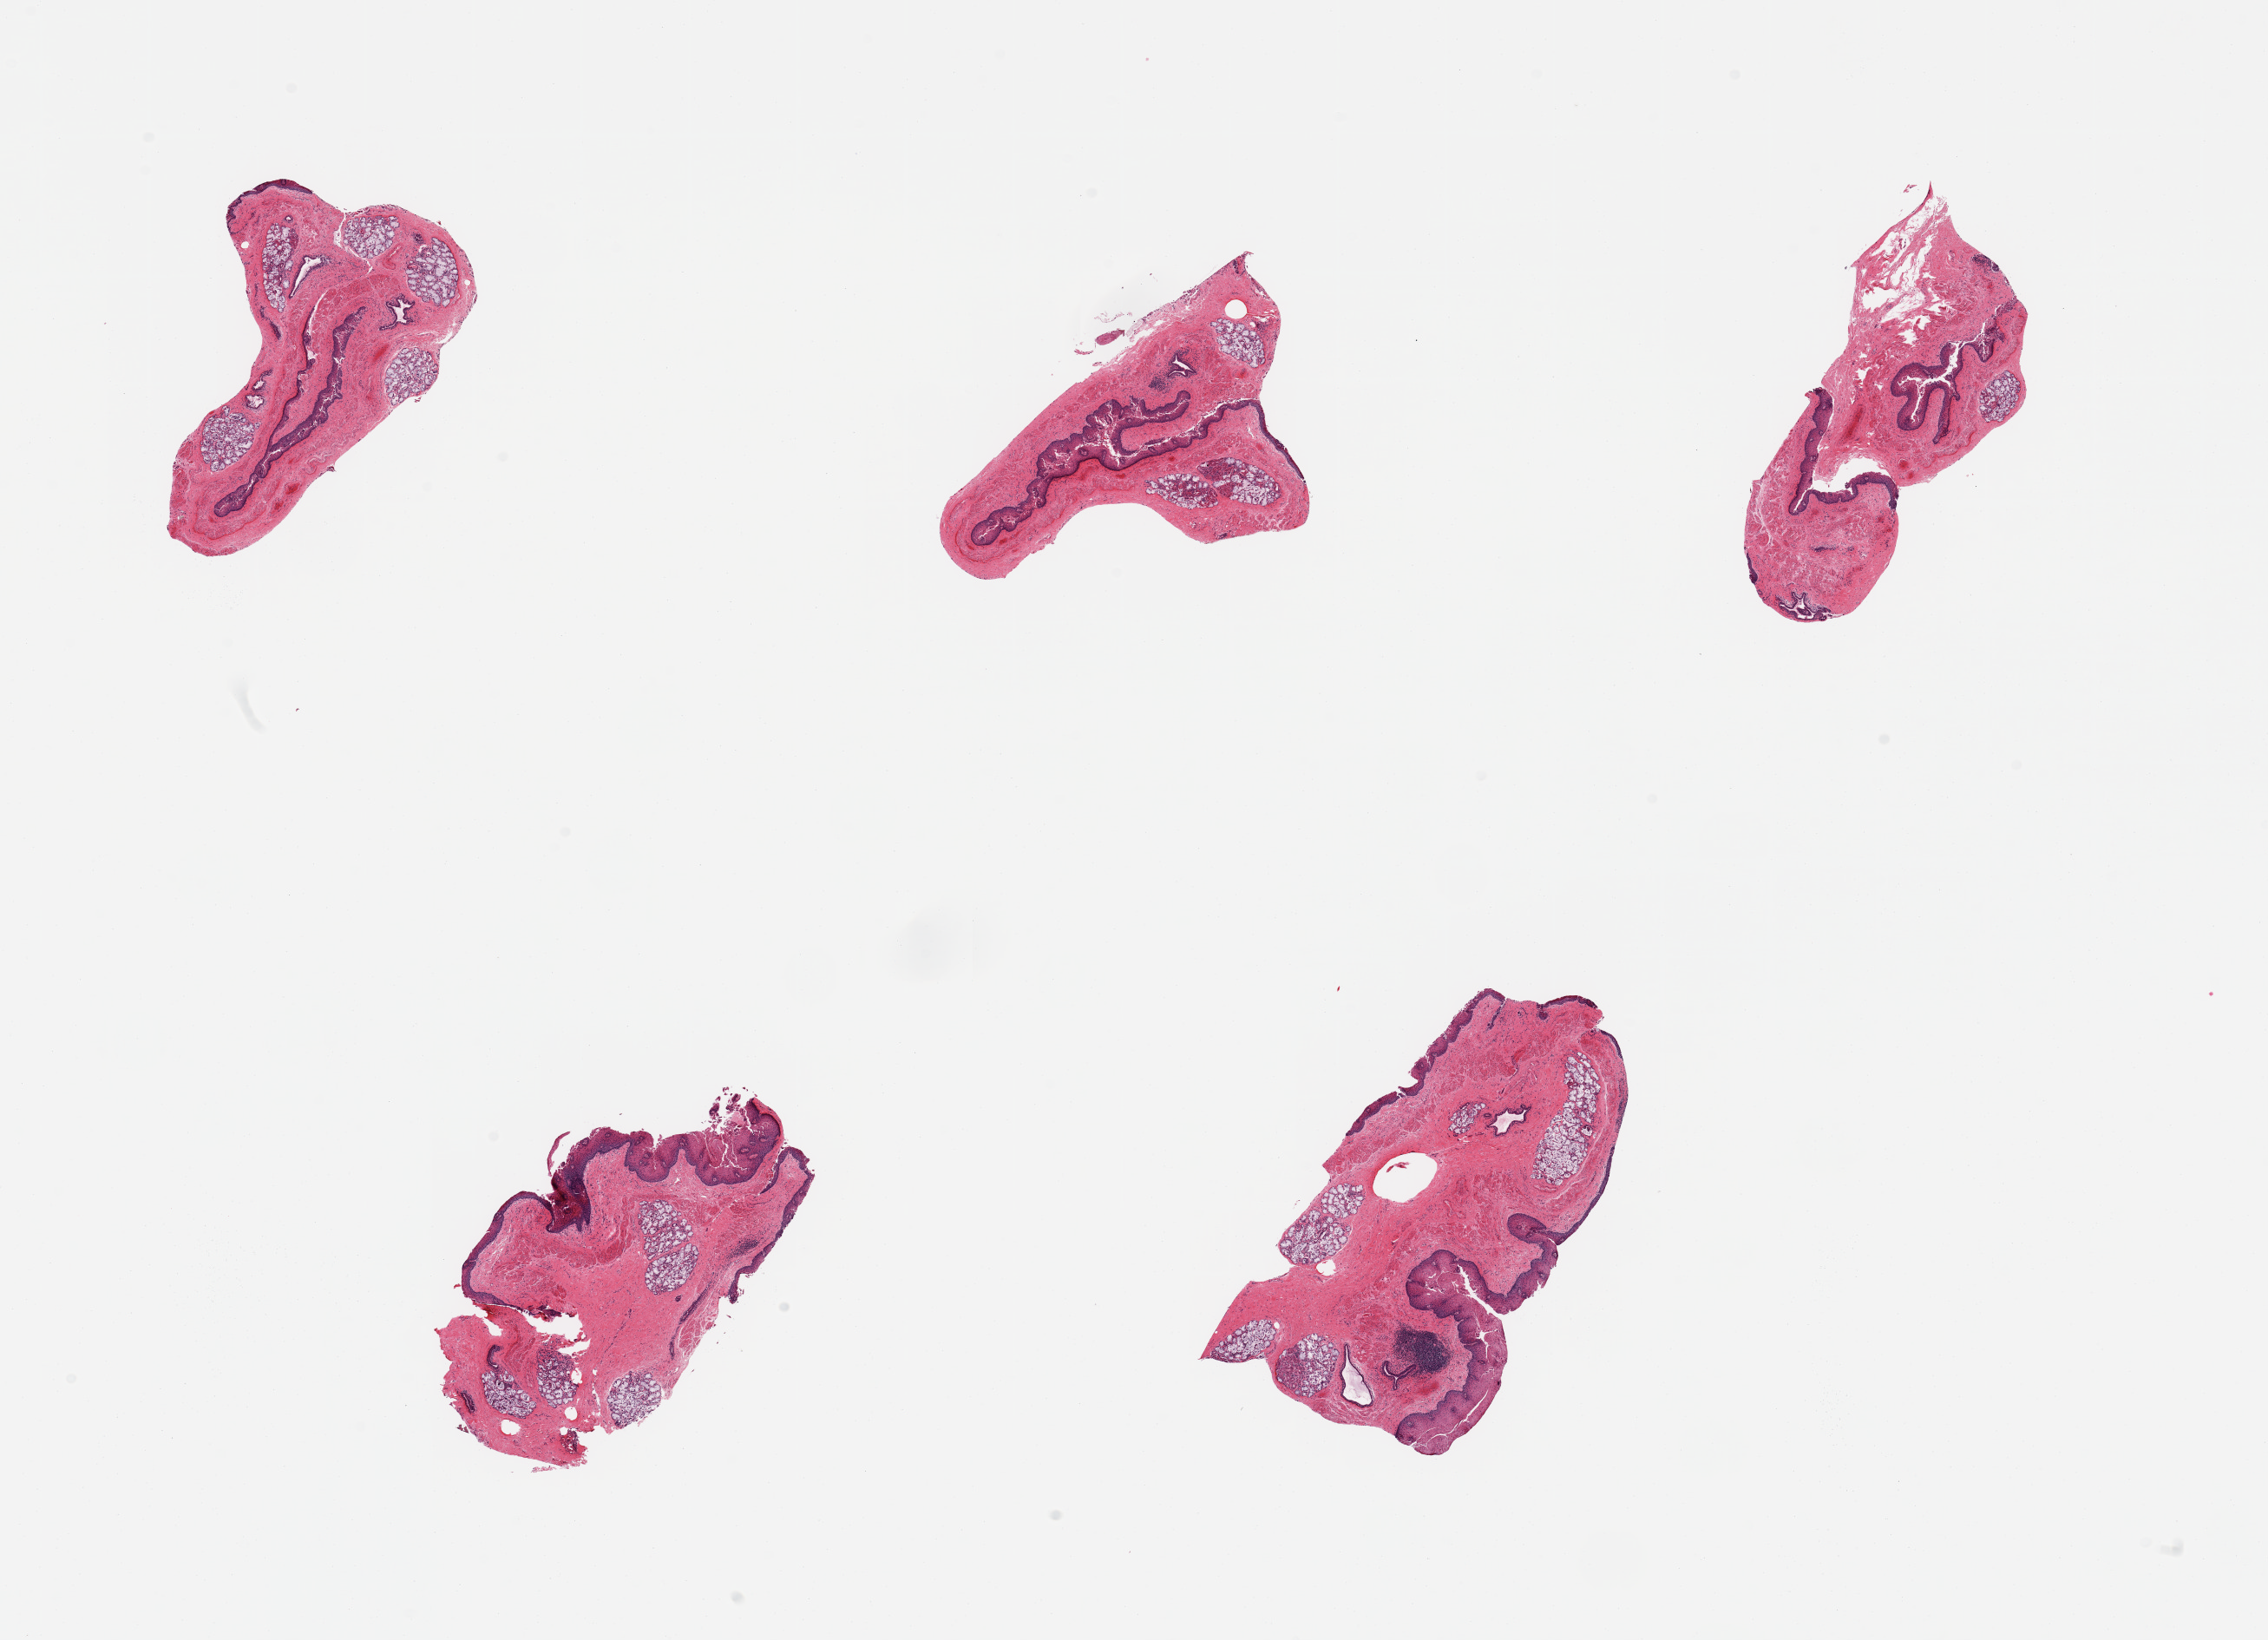
Whole-slide image, hematoxylin and eosin (H&E) stain, low-resolution overview of the scanned area, about 20.7 x 14.9 mm; PAXgene-fixed paraffin-embedded (PFPE) section; sampled site (target tissue): esophageal mucous membrane; donor tissue sample. Female donor.
* review note (as recorded): 5 pieces; partially sloughed epithelium; prominent submucosal glands comprise up to 20%